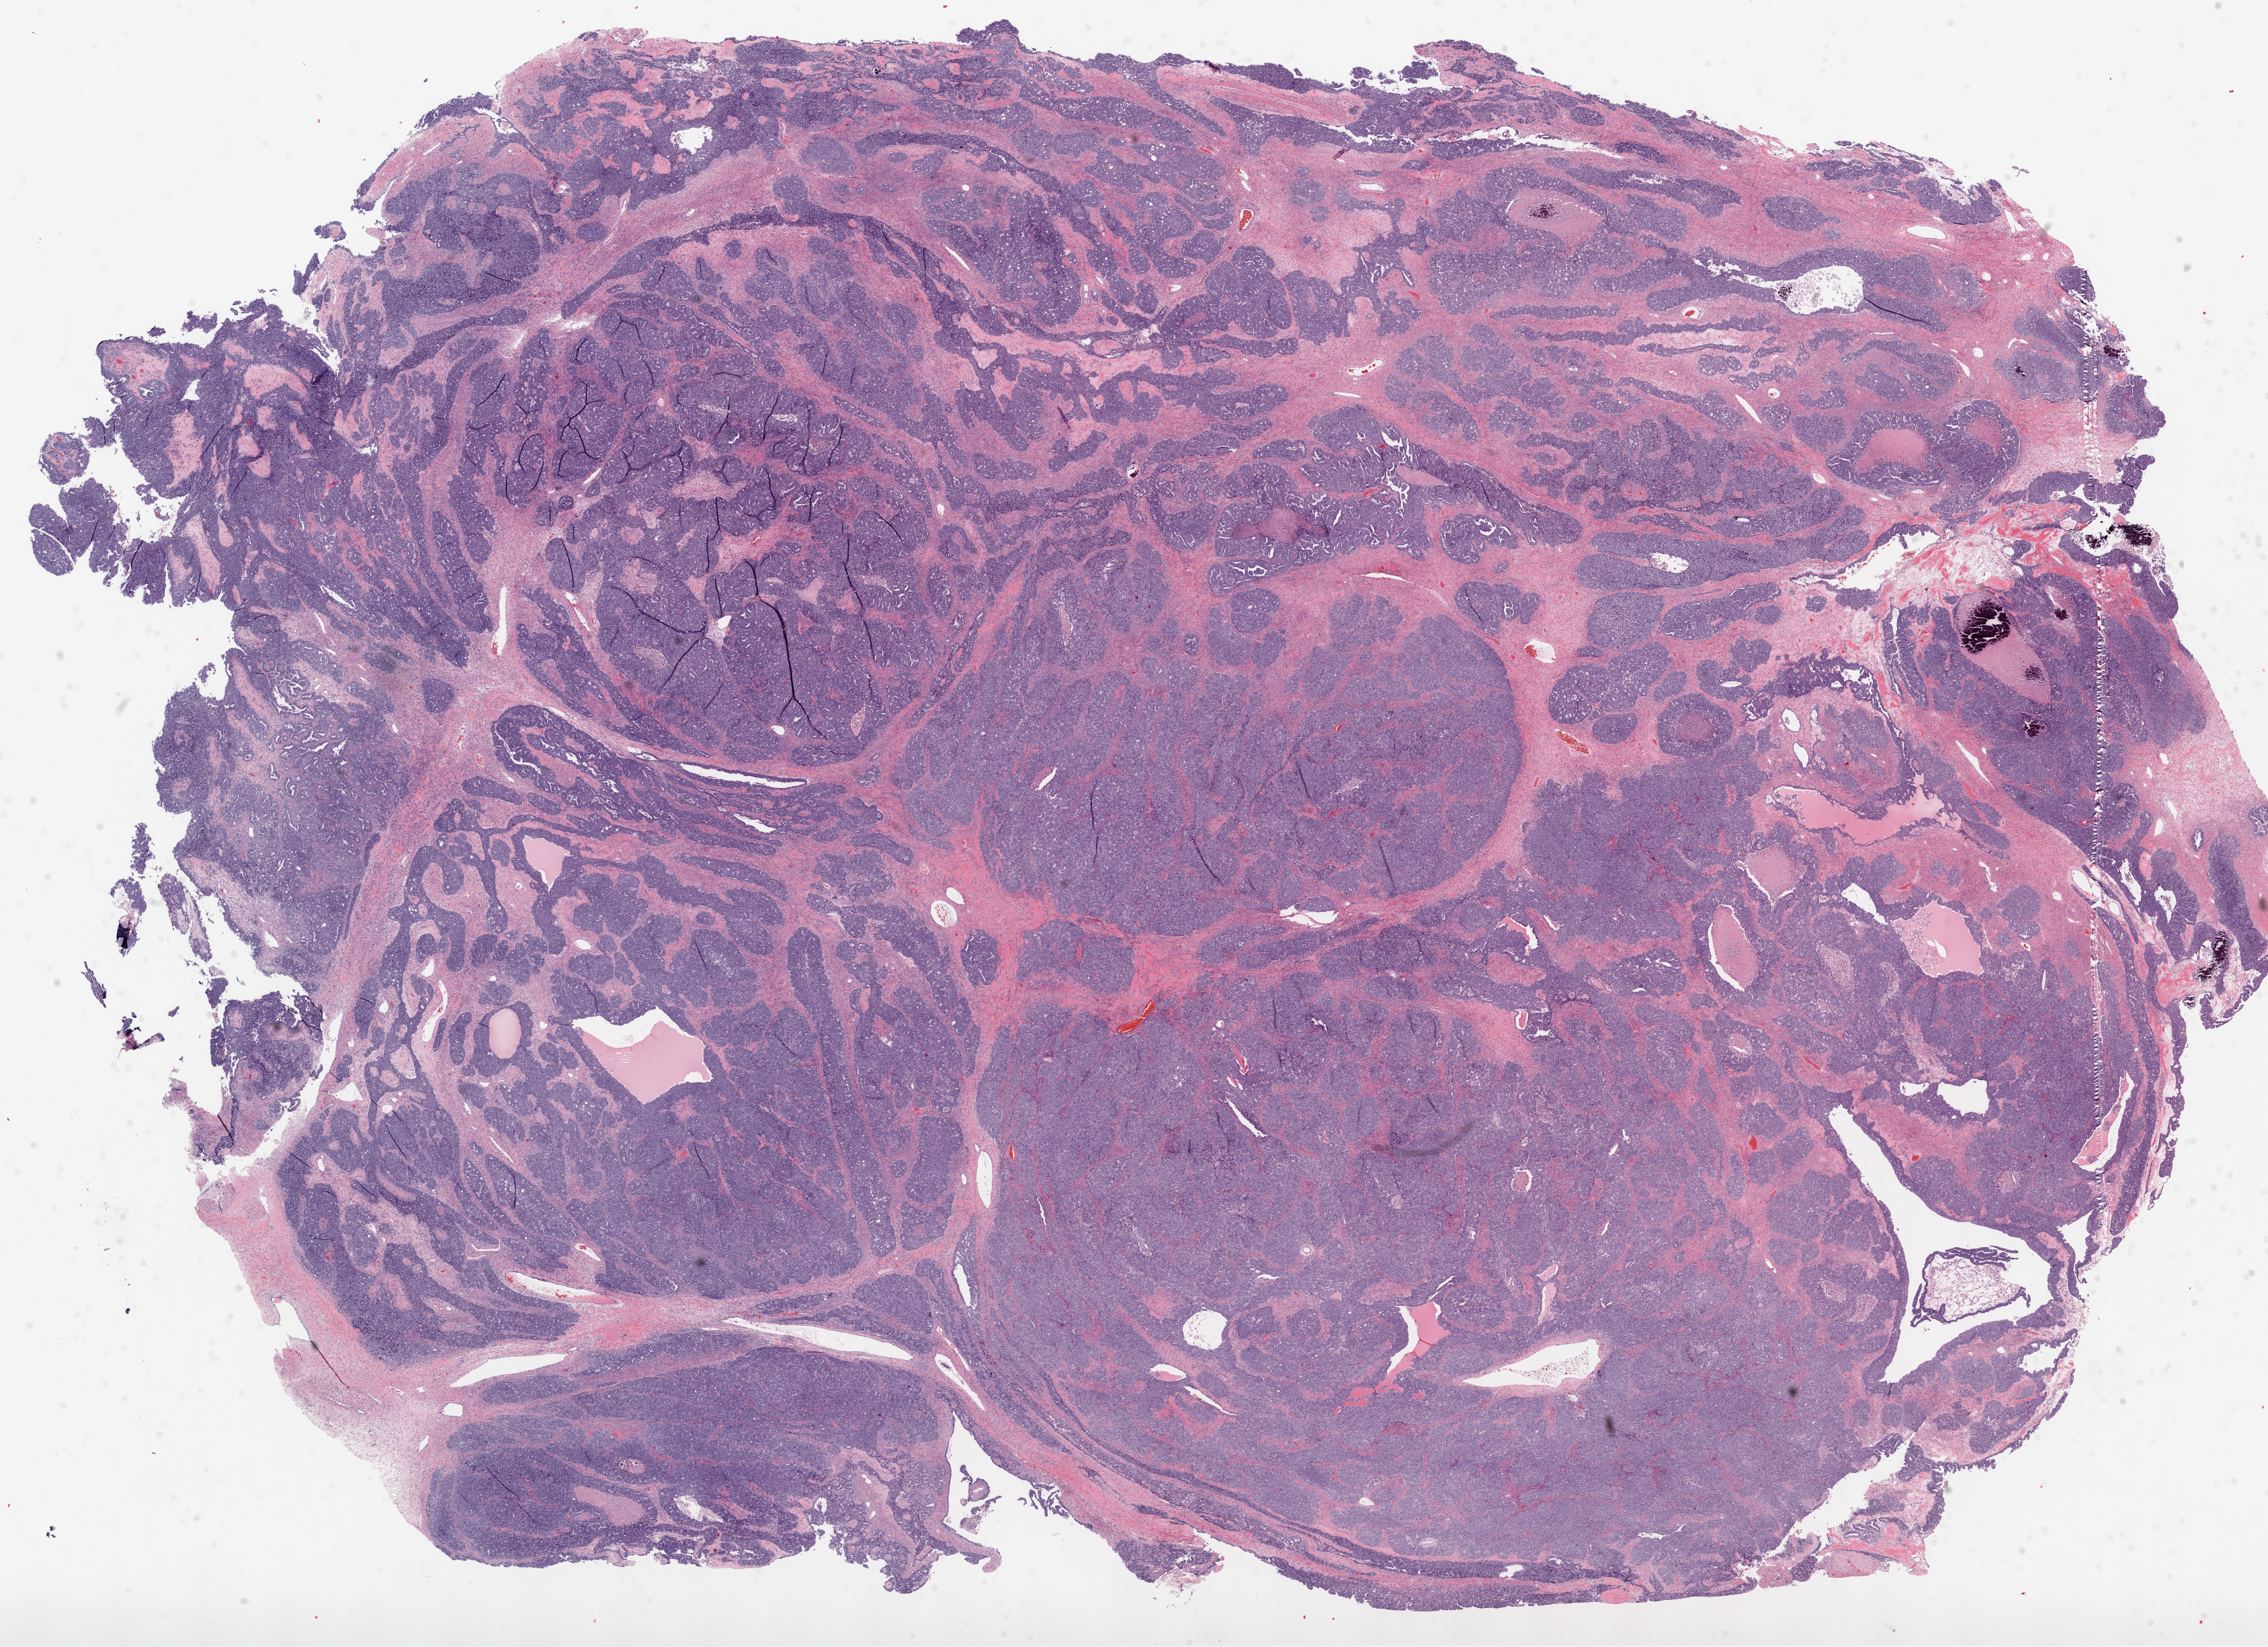
Whole-slide histology image, H&E-stained — whole scanned area (about 27.1 x 19.7 mm) shown as a low-resolution overview, frozen section from the top of the tissue portion, ovary, primary tumour sample. Female, age 64 years at initial diagnosis. Histologic grade: G3 (poorly differentiated). Composition of this section per pathologist review: tumour cells 75%, tumour nuclei 75%, normal cells 0%, stromal cells 20%, necrosis 5%.
* FIGO stage: IIIC
* laterality: left
* pathologic diagnosis: Serous cystadenocarcinoma, NOS